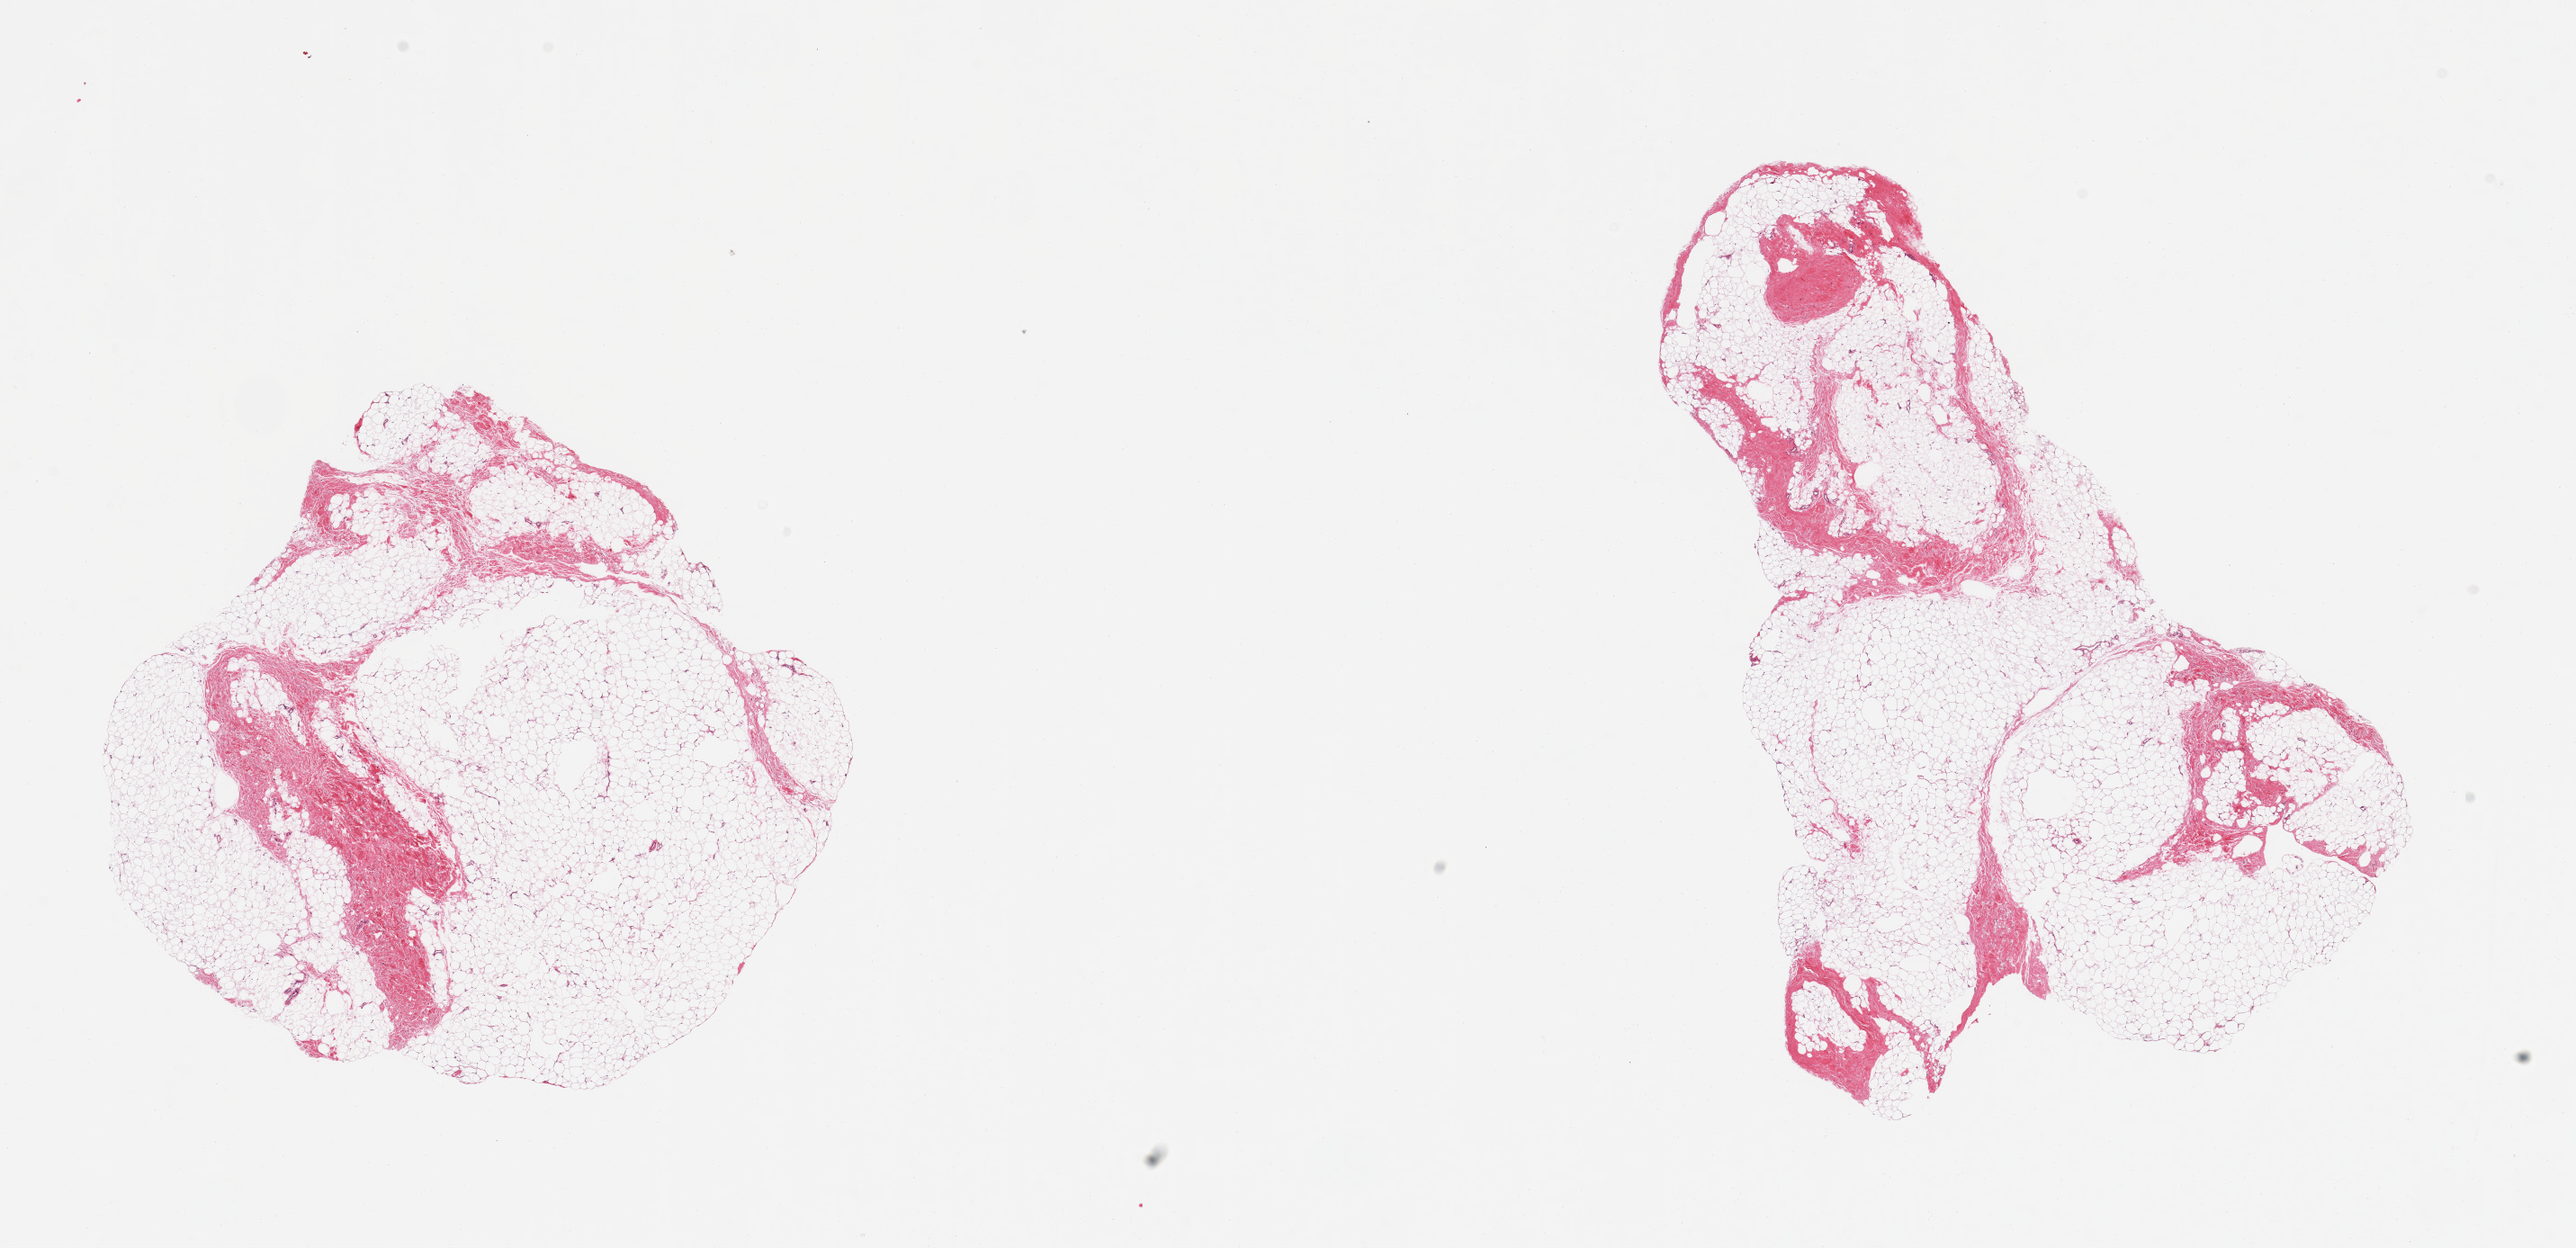
Digitized haematoxylin and eosin-stained section — a low-resolution overview of the entire scanned area, about 22.6 x 11.0 mm; PAXgene-fixed, paraffin-embedded tissue; target tissue: breast; tissue donor sample. Donor: male.
• pathologist's review note for this sample: 2 pieces; fibroadipose tissue devoid of ductal structures